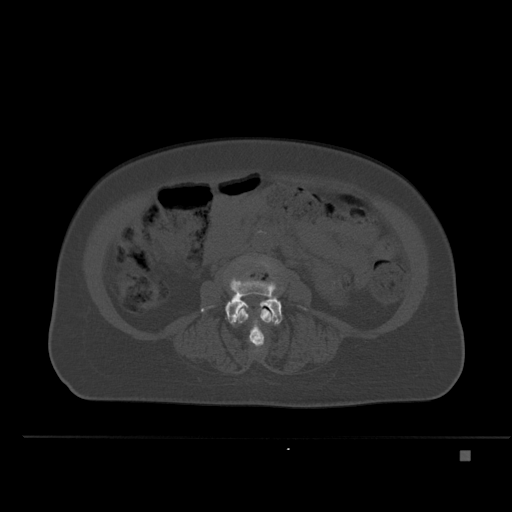
CT including the spine, one axial slice; slice 186 of 477 in the series (ordered by position); bone window (W 1800 / L 400 HU); 512 × 512 image matrix, field of view 422 × 422 mm. Female patient, age 74 years. From the clinical record (not read from this slice): primary cancer: colon.
Annotated regions visible in this slice (semi-automatically segmented with operator editing):
- L3 vertebra: bounding box (x1, y1, x2, y2) in pixels: (227, 258, 275, 348)
- L4 vertebra: (201, 279, 283, 326)